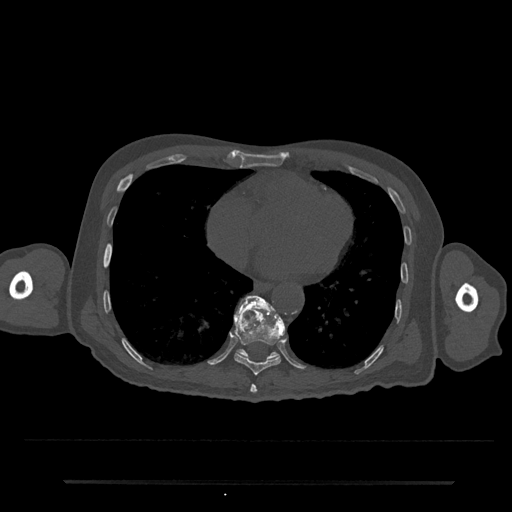
CT including the spine, one axial slice; slice 353 of 797 in the series (ordered by position); bone window (W 1800 / L 400 HU); 512 × 512 image matrix. Patient: male, 74 years. From the clinical record (not read from this slice): primary cancer: prostate.
Structures marked on this image (semi-automatically segmented with operator editing):
- T10 vertebra: bounding box <236,295,285,360> (left, top, right, bottom; pixels)
- T8 vertebra: <250,384,257,394>
- T9 vertebra: <234,296,285,375>